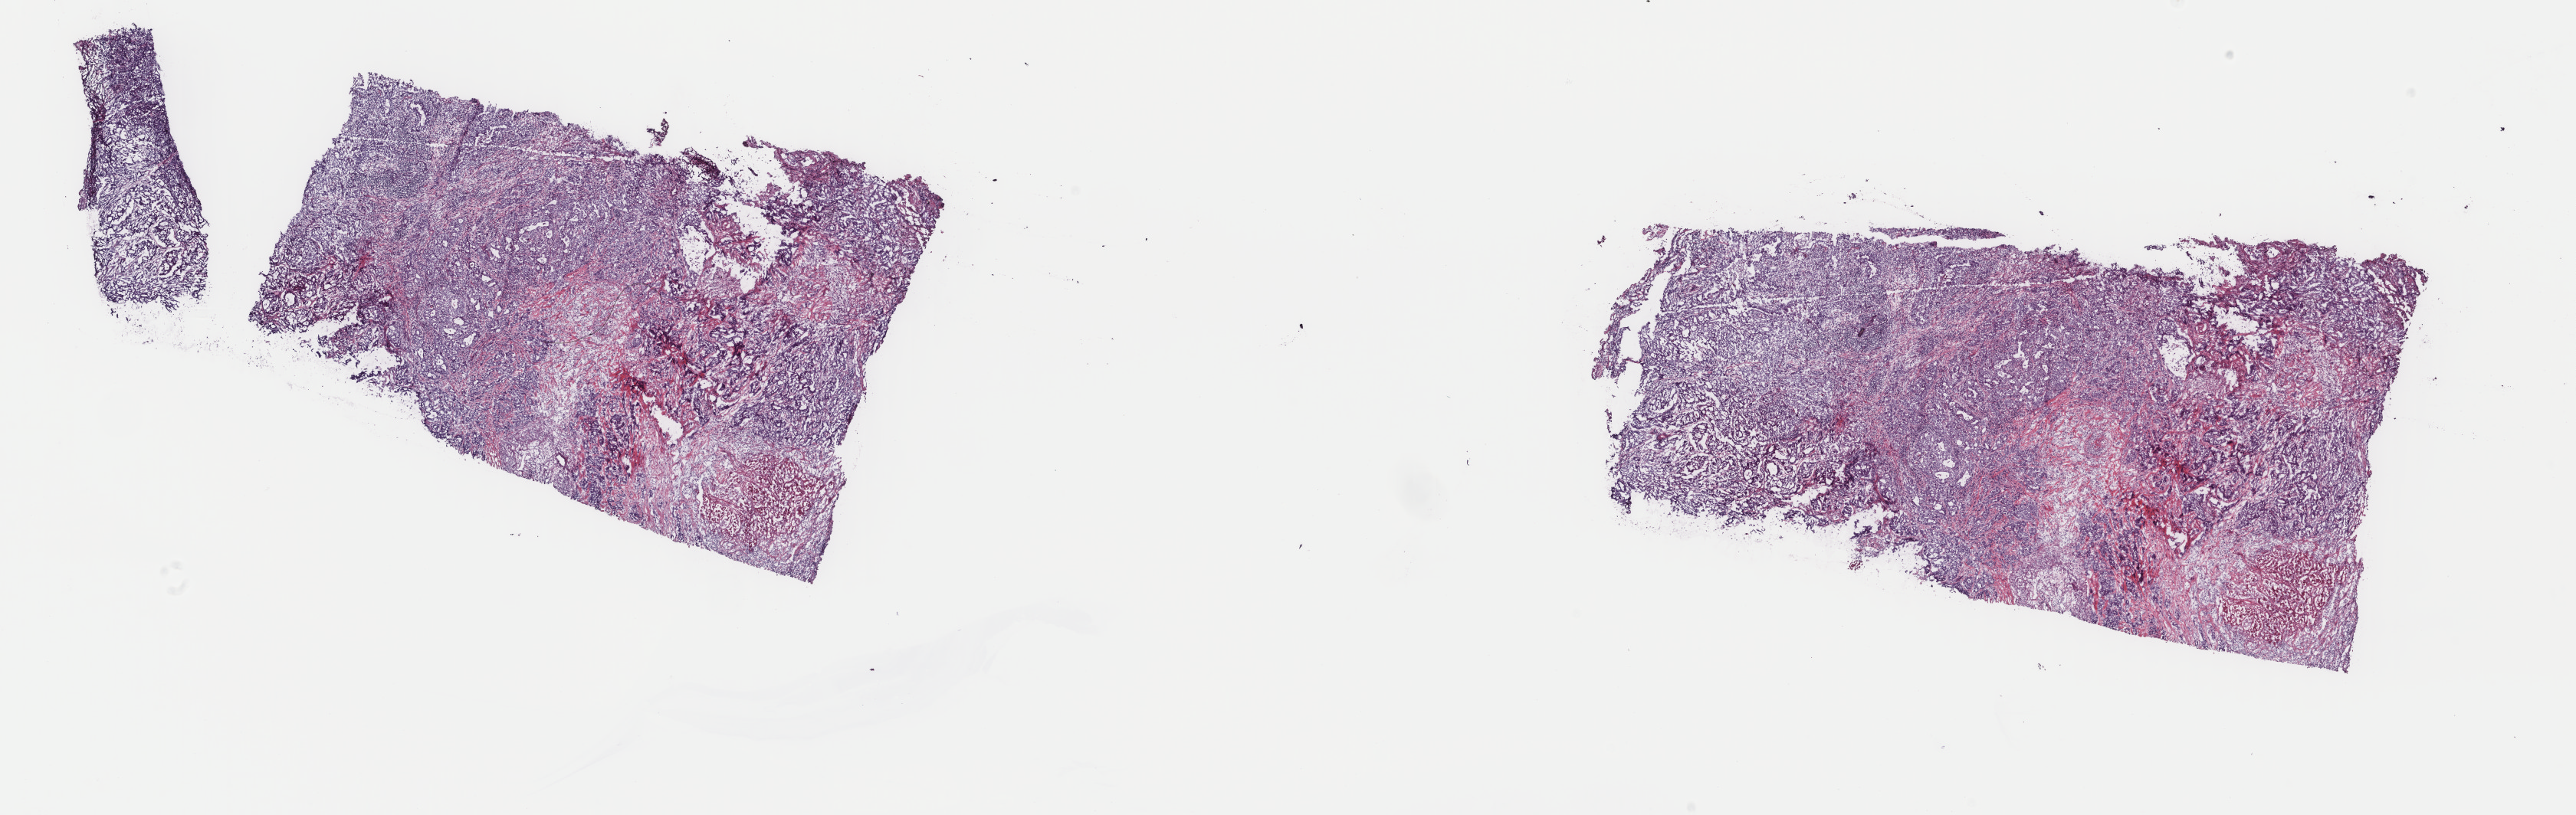
Hematoxylin and eosin (H&E) stained whole-slide image, whole scanned area (about 26.7 x 8.4 mm, from a 40x scan) shown as a low-resolution overview; frozen section; lung, primary tumour sample. Female patient; age at initial diagnosis 75 years. Composition of this section per pathologist review: tumour cells 92%, tumour nuclei 80%, normal cells 0%, stromal cells 5%, necrosis 3%. Infiltration values recorded for this section: lymphocyte infiltration 0%, monocyte infiltration 0%, neutrophil infiltration 0%.
Histologic diagnosis: Adenocarcinoma, NOS (upper lobe, lung). AJCC pathologic stage: IA (6th edition).